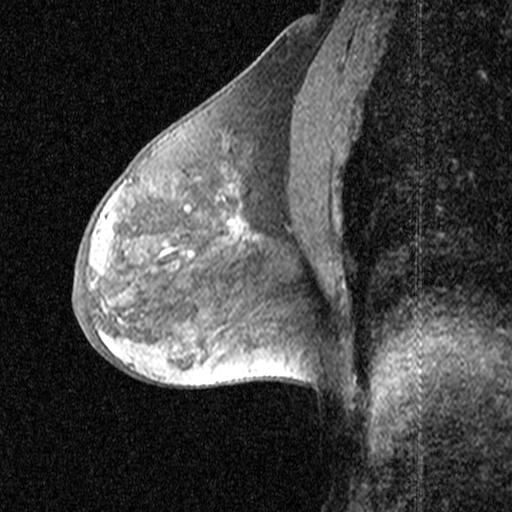
Breast MRI (dynamic contrast-enhanced), one sagittal slice; slice 24 of 44 in the series (ordered by position); dynamic contrast-enhanced study with each time point stored as its own series, time point 2 of 3 at this slice position (early post-contrast, ordered by acquisition time); 1.5 T; TE 4.5 ms, TR 11 ms; 512 × 512 image matrix. Female patient, age 53 years. Case-level facts recorded for this patient, not image findings: setting: breast cancer imaged before/during neoadjuvant chemotherapy; receptor status: HR-positive, HER2-negative.
Annotated regions visible in this slice (semi-automatically segmented with operator editing):
- analysis volume of interest (the breast-tissue region the enhancement analysis was run in; not a lesion): box from (x=198, y=152) to (x=299, y=267) px
- tumour enhancement mask (voxels above the 90 % enhancement threshold inside the analysis volume of interest): (x=231, y=220)–(x=236, y=224)